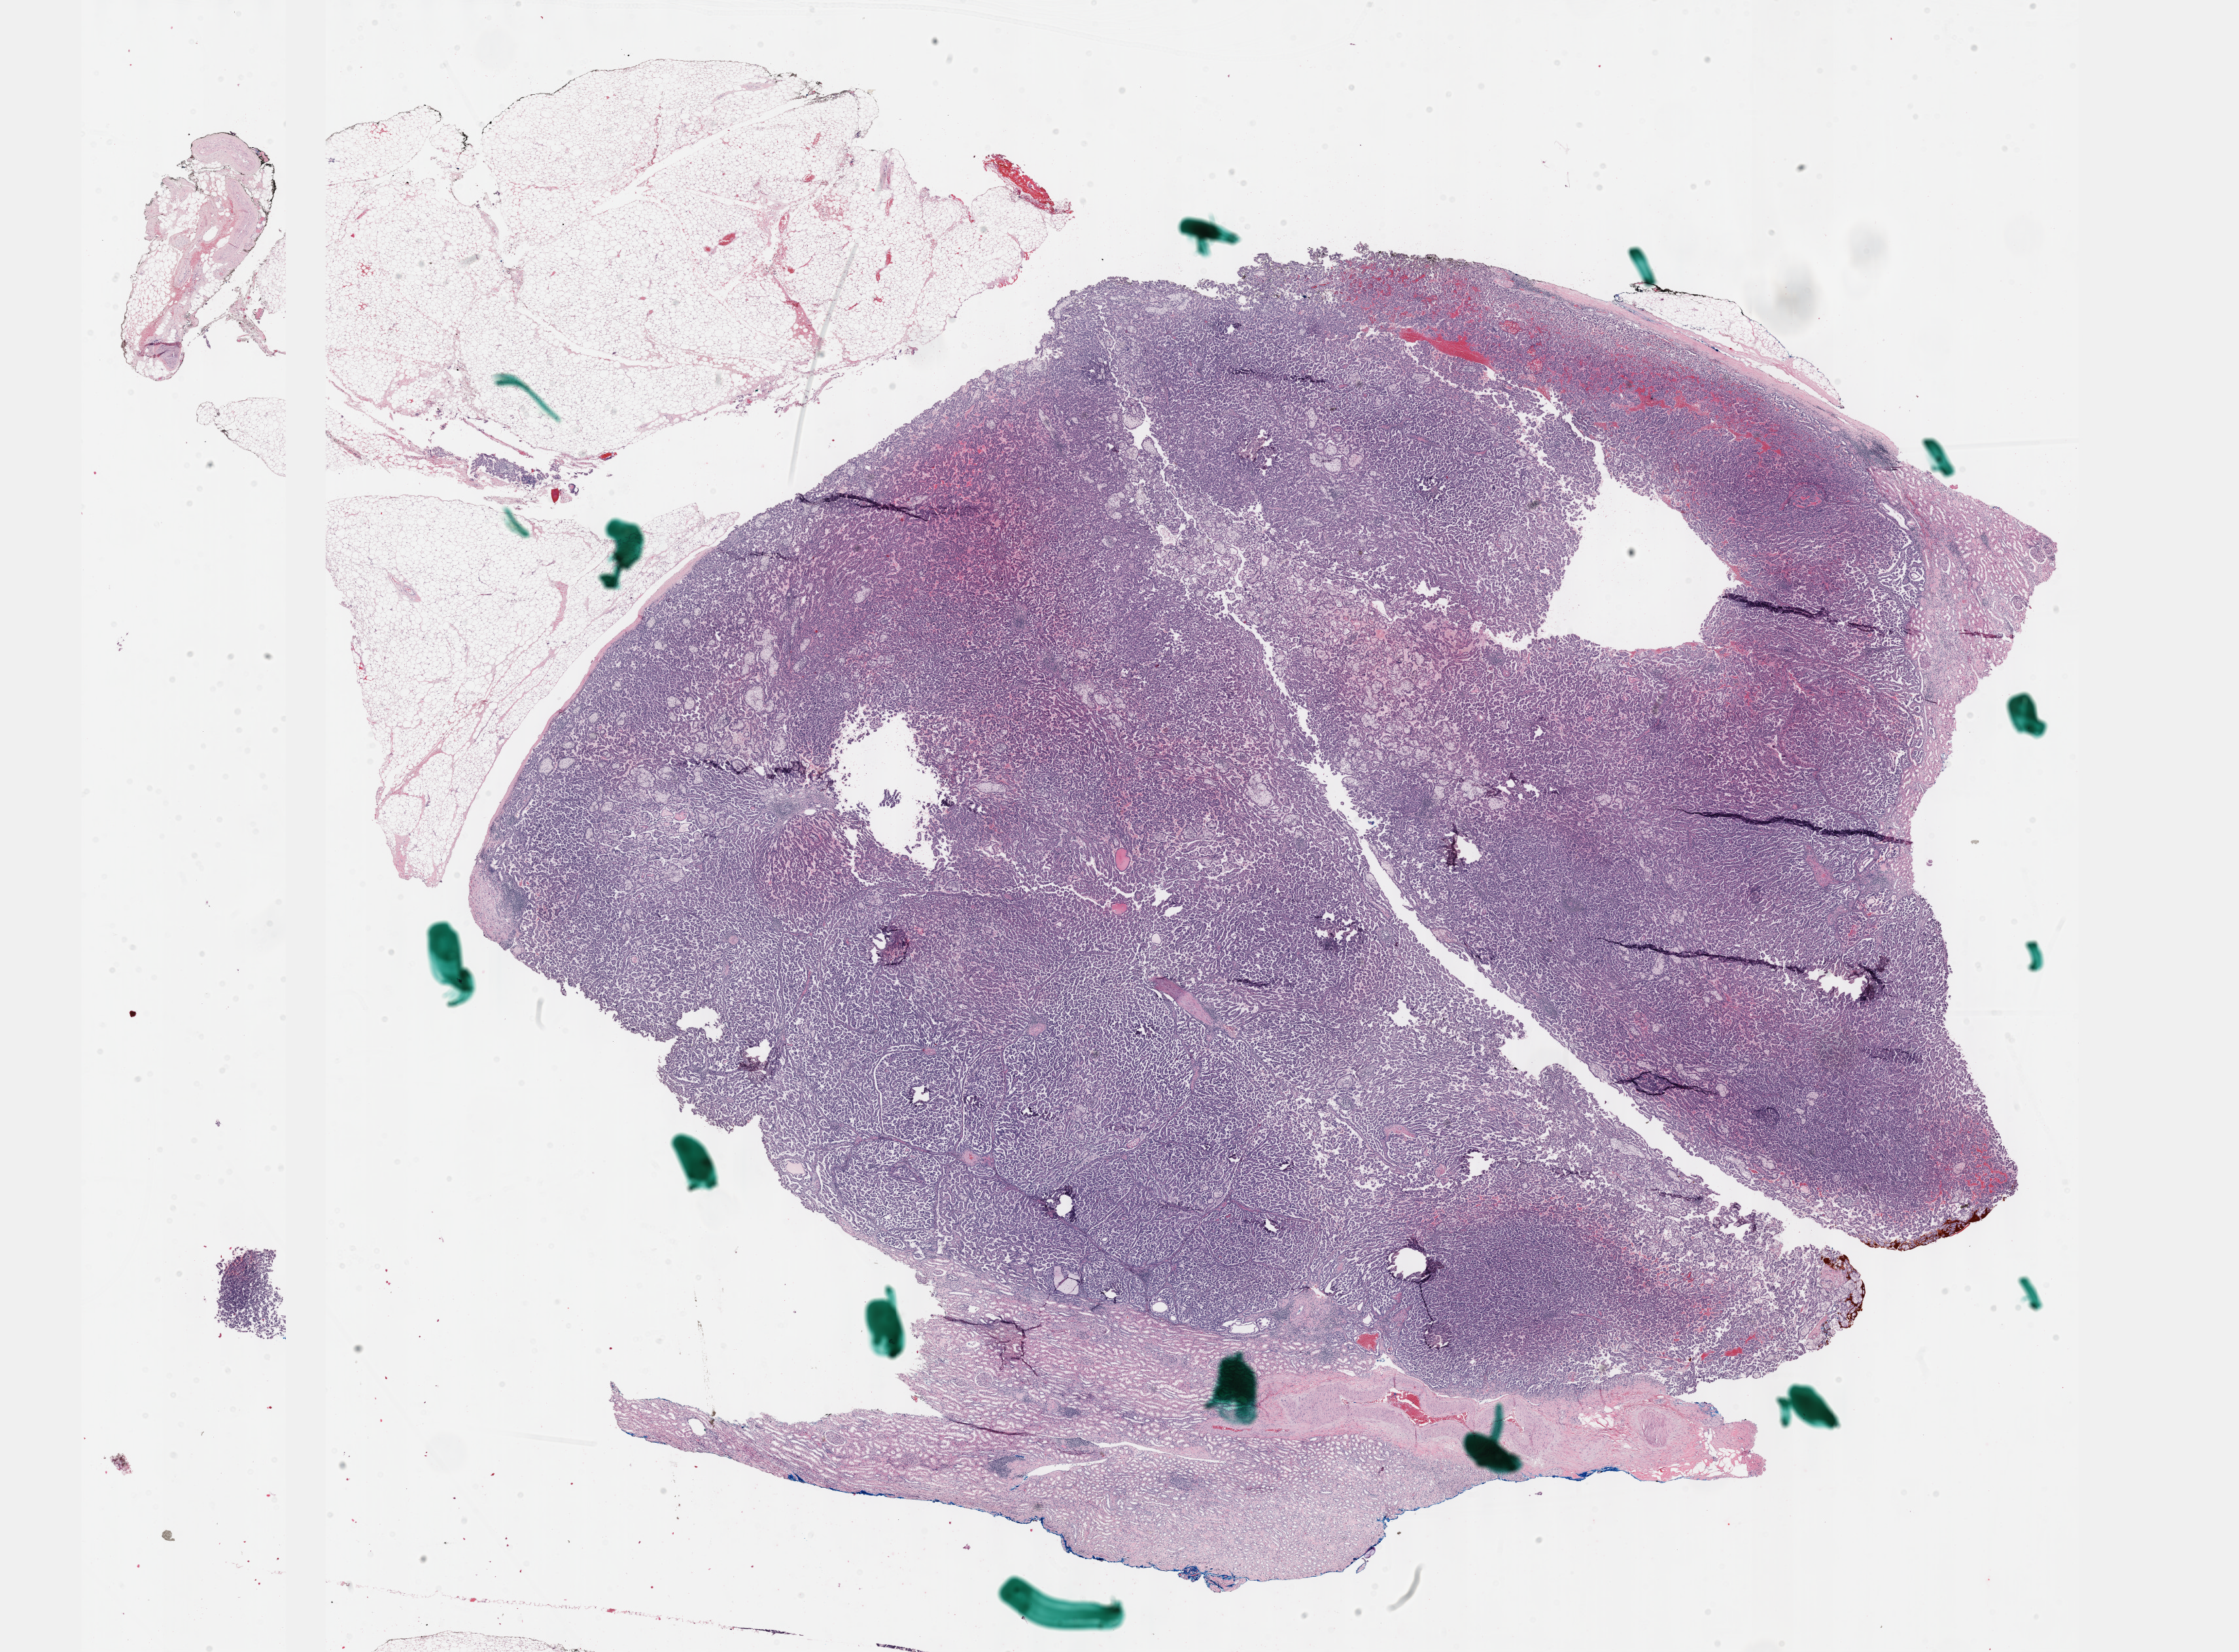
H&E whole-slide image — low-resolution overview of the scanned area, about 27.7 x 20.4 mm (slide scanned at 40x); formalin-fixed paraffin-embedded (FFPE) diagnostic section; kidney, primary tumour sample. Patient: male, age at initial diagnosis 65 years.
Diagnosis: Papillary adenocarcinoma, NOS.